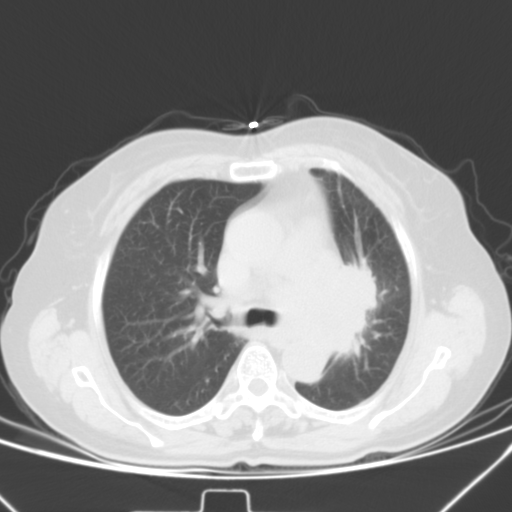
Chest CT, one axial slice. Position 28 of 42 along the scan axis. Lung window (W 1500 / L -600 HU). 5 mm slice thickness. 512 × 512 image matrix, field of view 331 × 331 mm. Patient: female, 59 years. From the clinical record (not read from this slice): clinical TNM (as recorded): T3 N1 M0; histopathological grade: G3.
Annotated regions visible in this slice (rectangle marked by the reading radiologist):
- lung tumour (recorded histology: small cell carcinoma): bounding box (x1, y1, x2, y2) in pixels: (321, 233, 378, 365)